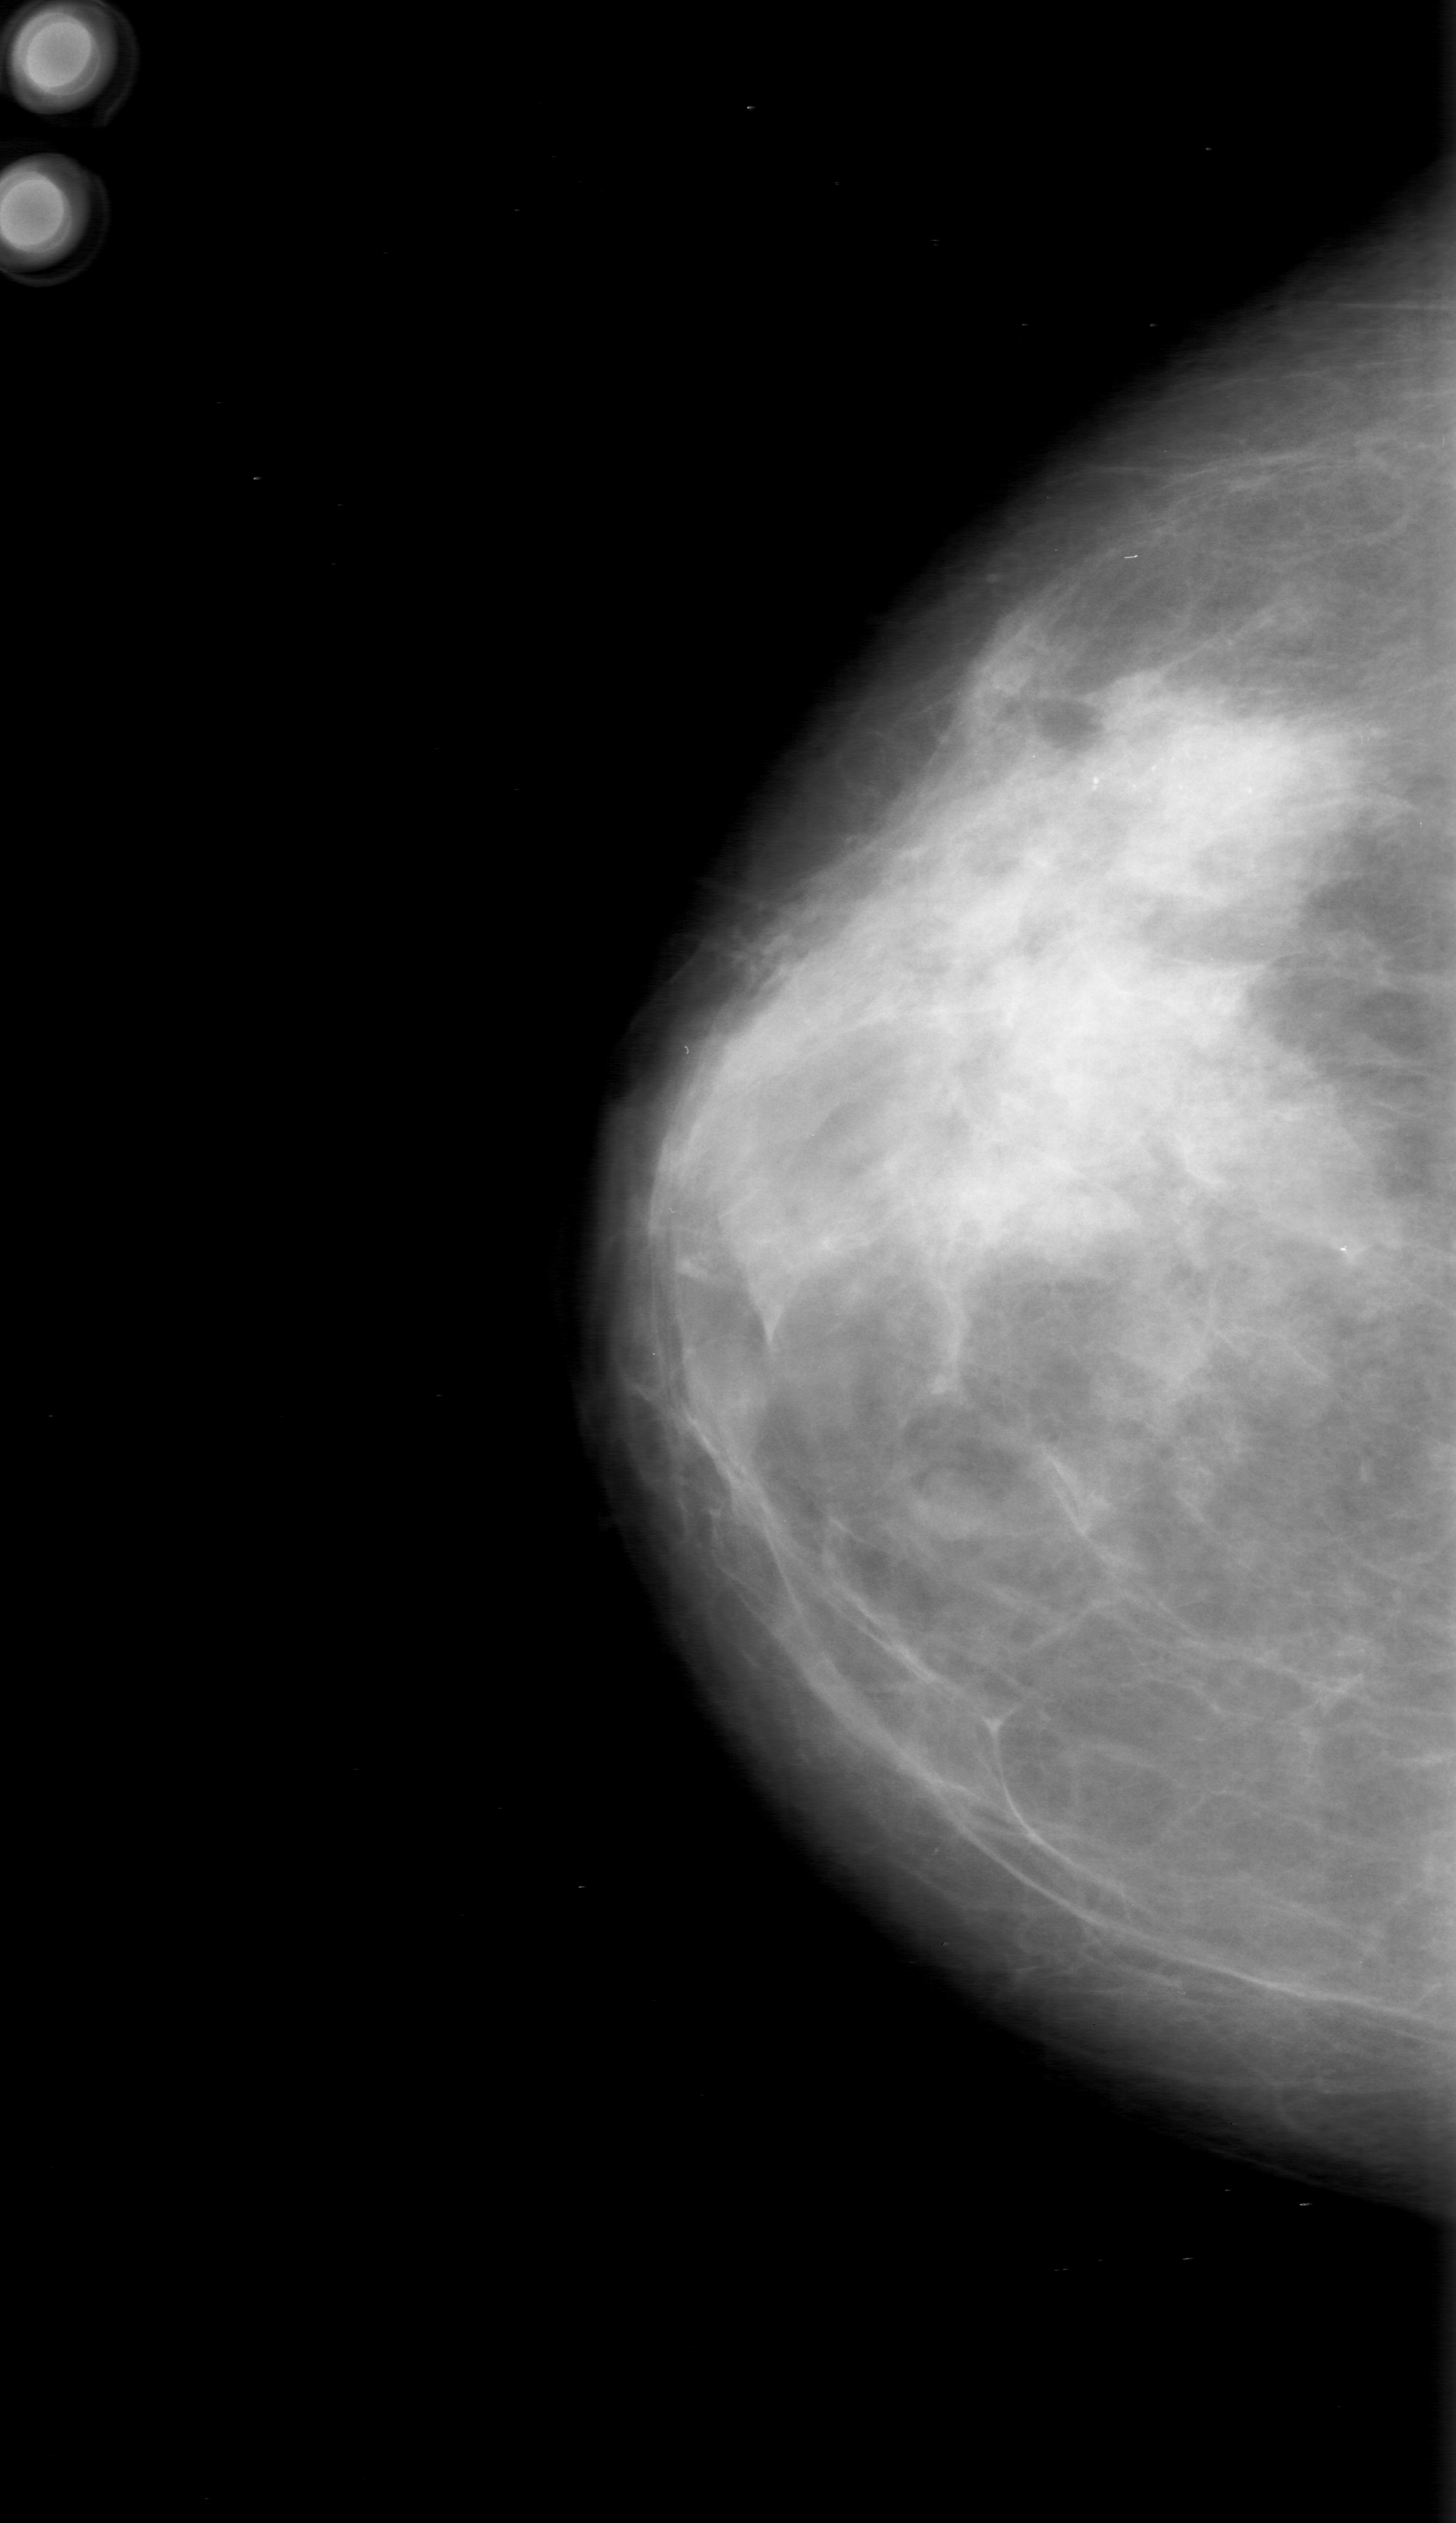
Scanned film-screen mammogram, right breast, CC view, BI-RADS breast density category 3 (scale 1–4).
Radiologist-marked abnormalities on this image: calcifications, morphology pleomorphic, distribution clustered; BI-RADS assessment category 0 (incomplete: needs additional imaging); pathology result (as recorded, not read from the image): malignant.